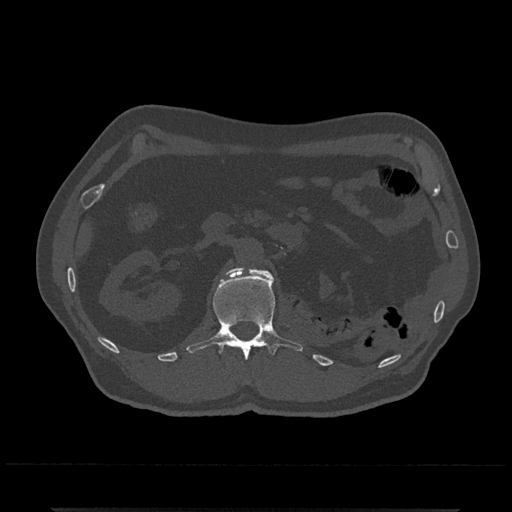
CT including the spine, one axial slice; slice 358 of 797 in the series (ordered by position); 120 kVp; bone window (W 1800 / L 400 HU); 512 × 512 image matrix, field of view 393 × 393 mm. Male patient, age 67 years. Case-level facts recorded for this patient, not image findings: primary cancer: prostate.
Annotated regions visible in this slice (semi-automatic segmentation, software-assisted and operator-edited):
- L1 vertebra: bounding box [x1, y1, x2, y2] px = [186, 267, 303, 361]